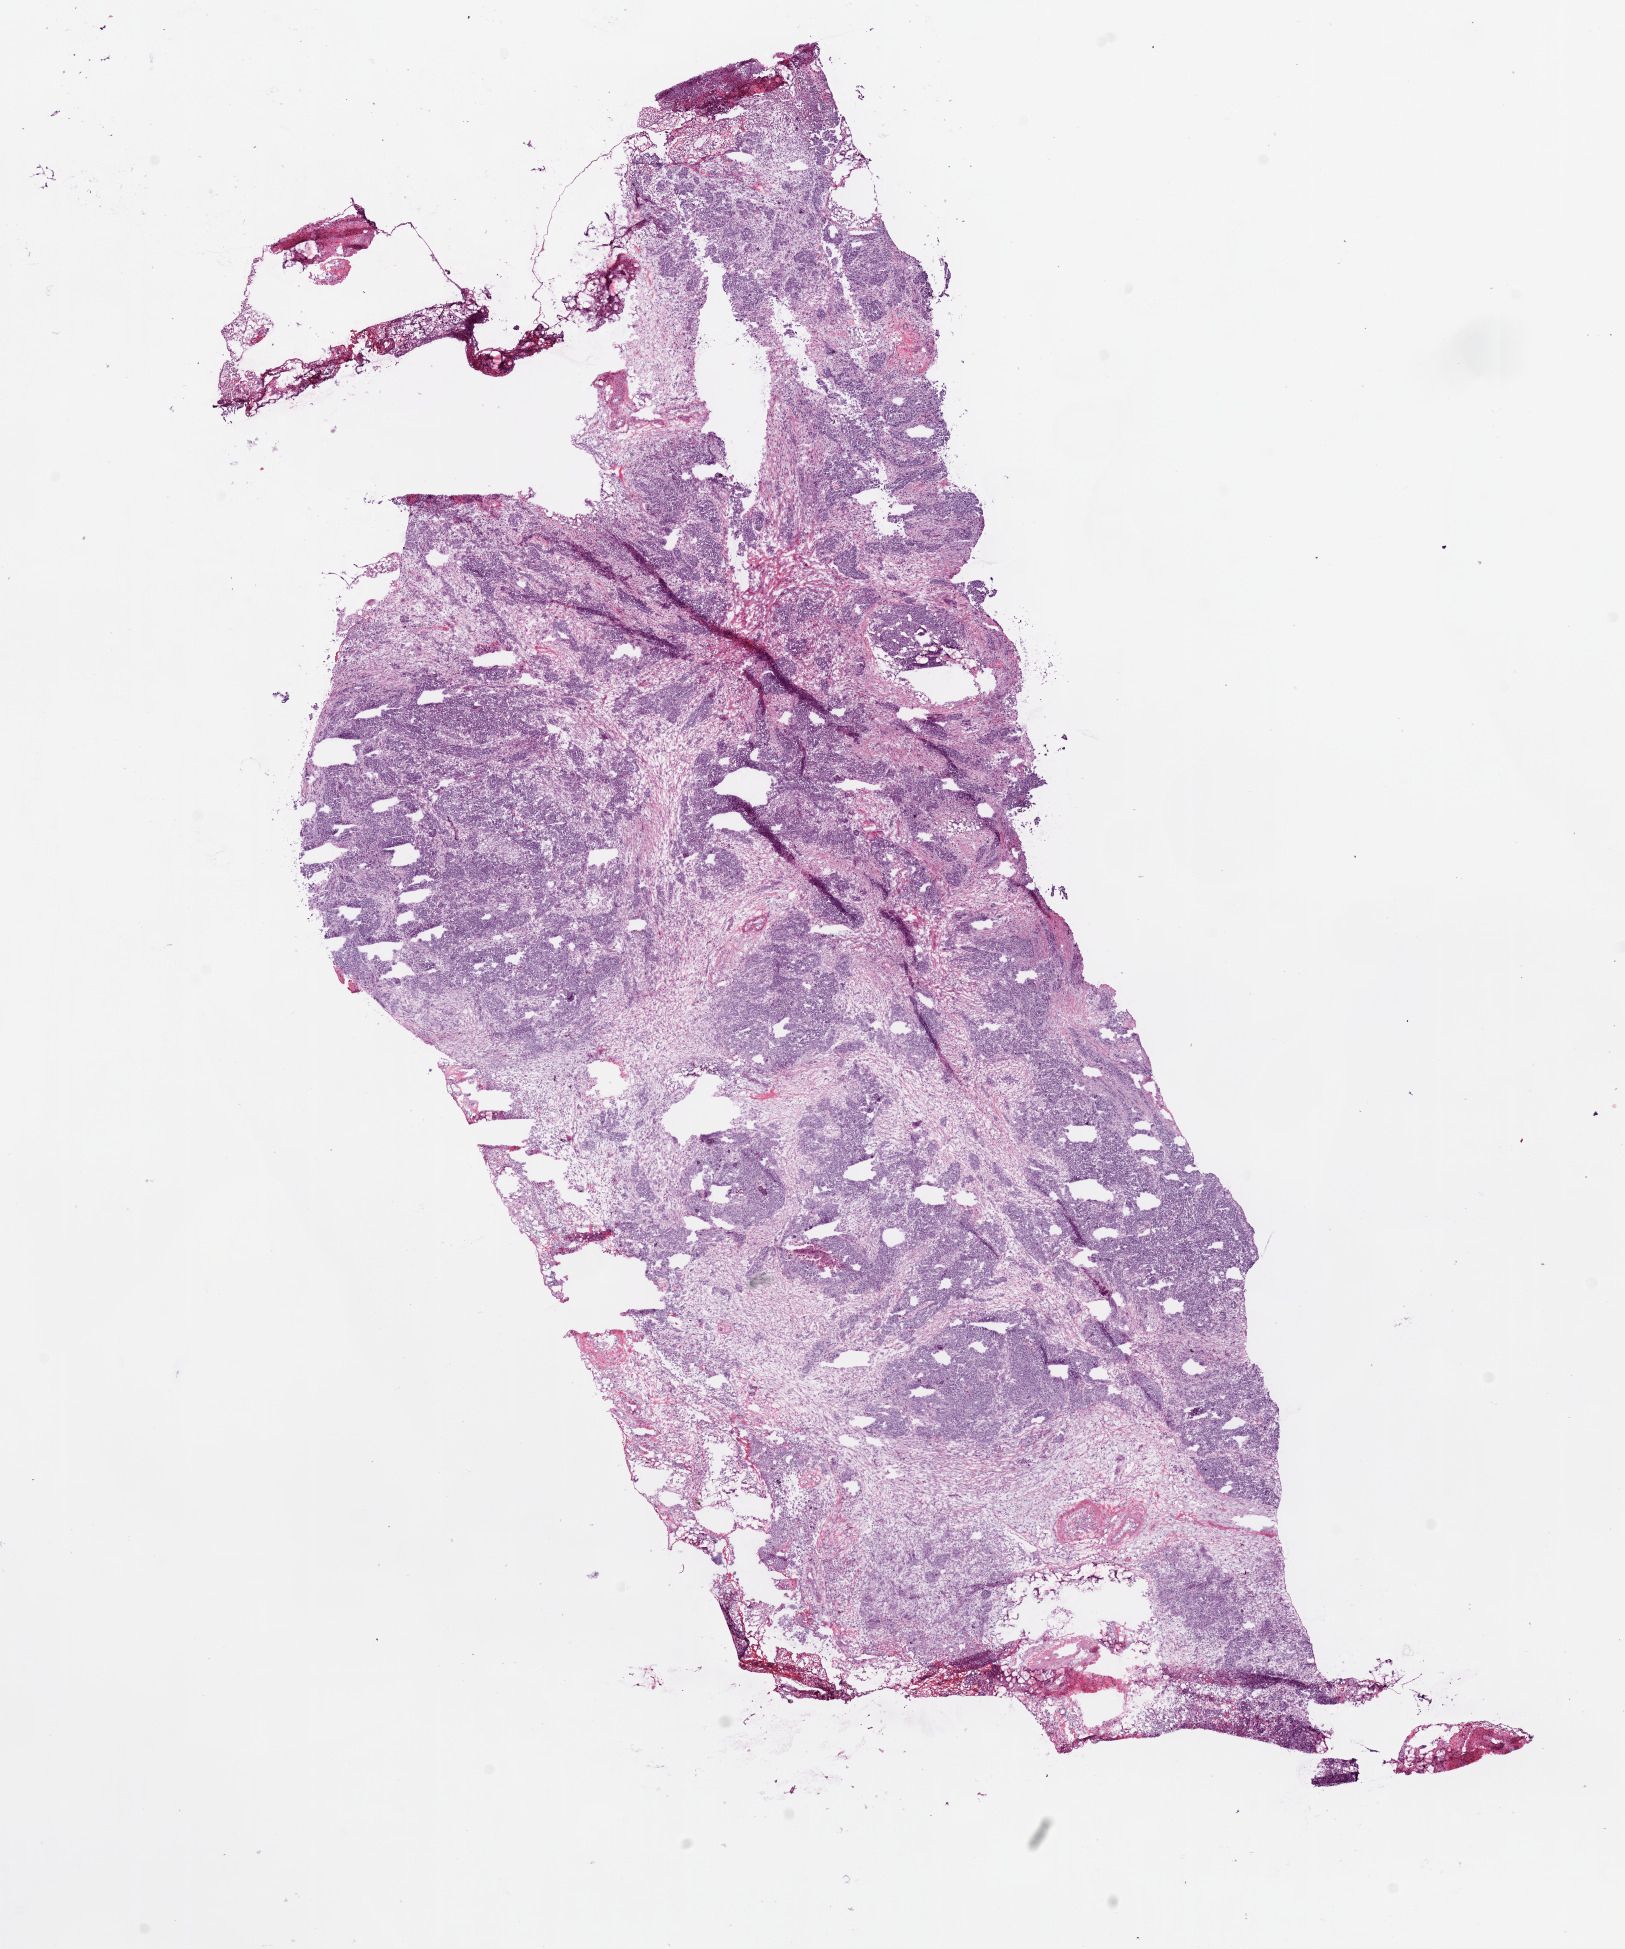
Digitized H&E tissue section (whole slide) — low-resolution overview of the scanned area, about 13.0 x 15.6 mm. Frozen section from the top of the tissue portion. Sample: primary tumour, ovary. Female patient; age at initial diagnosis 71 years. Histologic grade: G3 (poorly differentiated). Slide review estimates, as recorded: tumour cells 55%, tumour nuclei 75%, normal cells 0%, stromal cells 40%, necrosis 5%.
Histologic diagnosis: Serous cystadenocarcinoma, NOS. FIGO stage: IIIC.